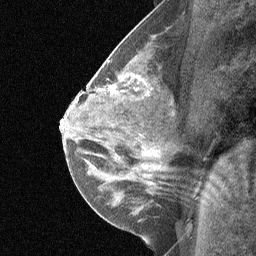
Breast MRI (dynamic contrast-enhanced), one sagittal slice. Position 35 of 64 along the scan axis. Dynamic contrast-enhanced study with each time point stored as its own series, time point 3 of 5 at this slice position (ordered by acquisition time). 1.5 T. TE 4.8 ms, TR 27 ms. 2 mm slice thickness. 256 × 256 image matrix, field of view 180 × 180 mm. Female patient, age 26 years. From the clinical record (not read from this slice): setting: breast cancer imaged before/during neoadjuvant chemotherapy; receptor status: HR-positive, HER2-negative.
Annotated regions visible in this slice (semi-automatically segmented with operator editing):
- analysis volume of interest (the breast-tissue region the enhancement analysis was run in; not a lesion): box from (x=85, y=46) to (x=175, y=144) px
- tumour enhancement mask (voxels above the 90 % enhancement threshold inside the analysis volume of interest): (x=110, y=76)–(x=140, y=90)